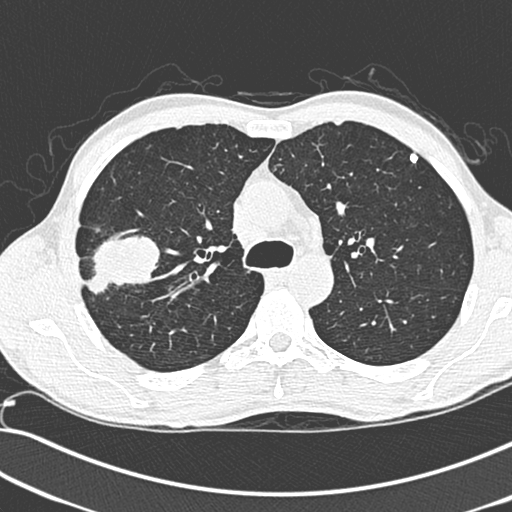
Low-dose screening chest CT, one axial slice; slice 205 of 281 in the series (ordered by position); lung window (W 1500 / L -600 HU); 512 × 512 image matrix, field of view 341 × 341 mm.
Annotated regions visible in this slice (expert manual segmentation):
- lesion 1 (tumor, upper lobe of right lung): bounding box (x1, y1, x2, y2) in pixels: (86, 233, 160, 299)